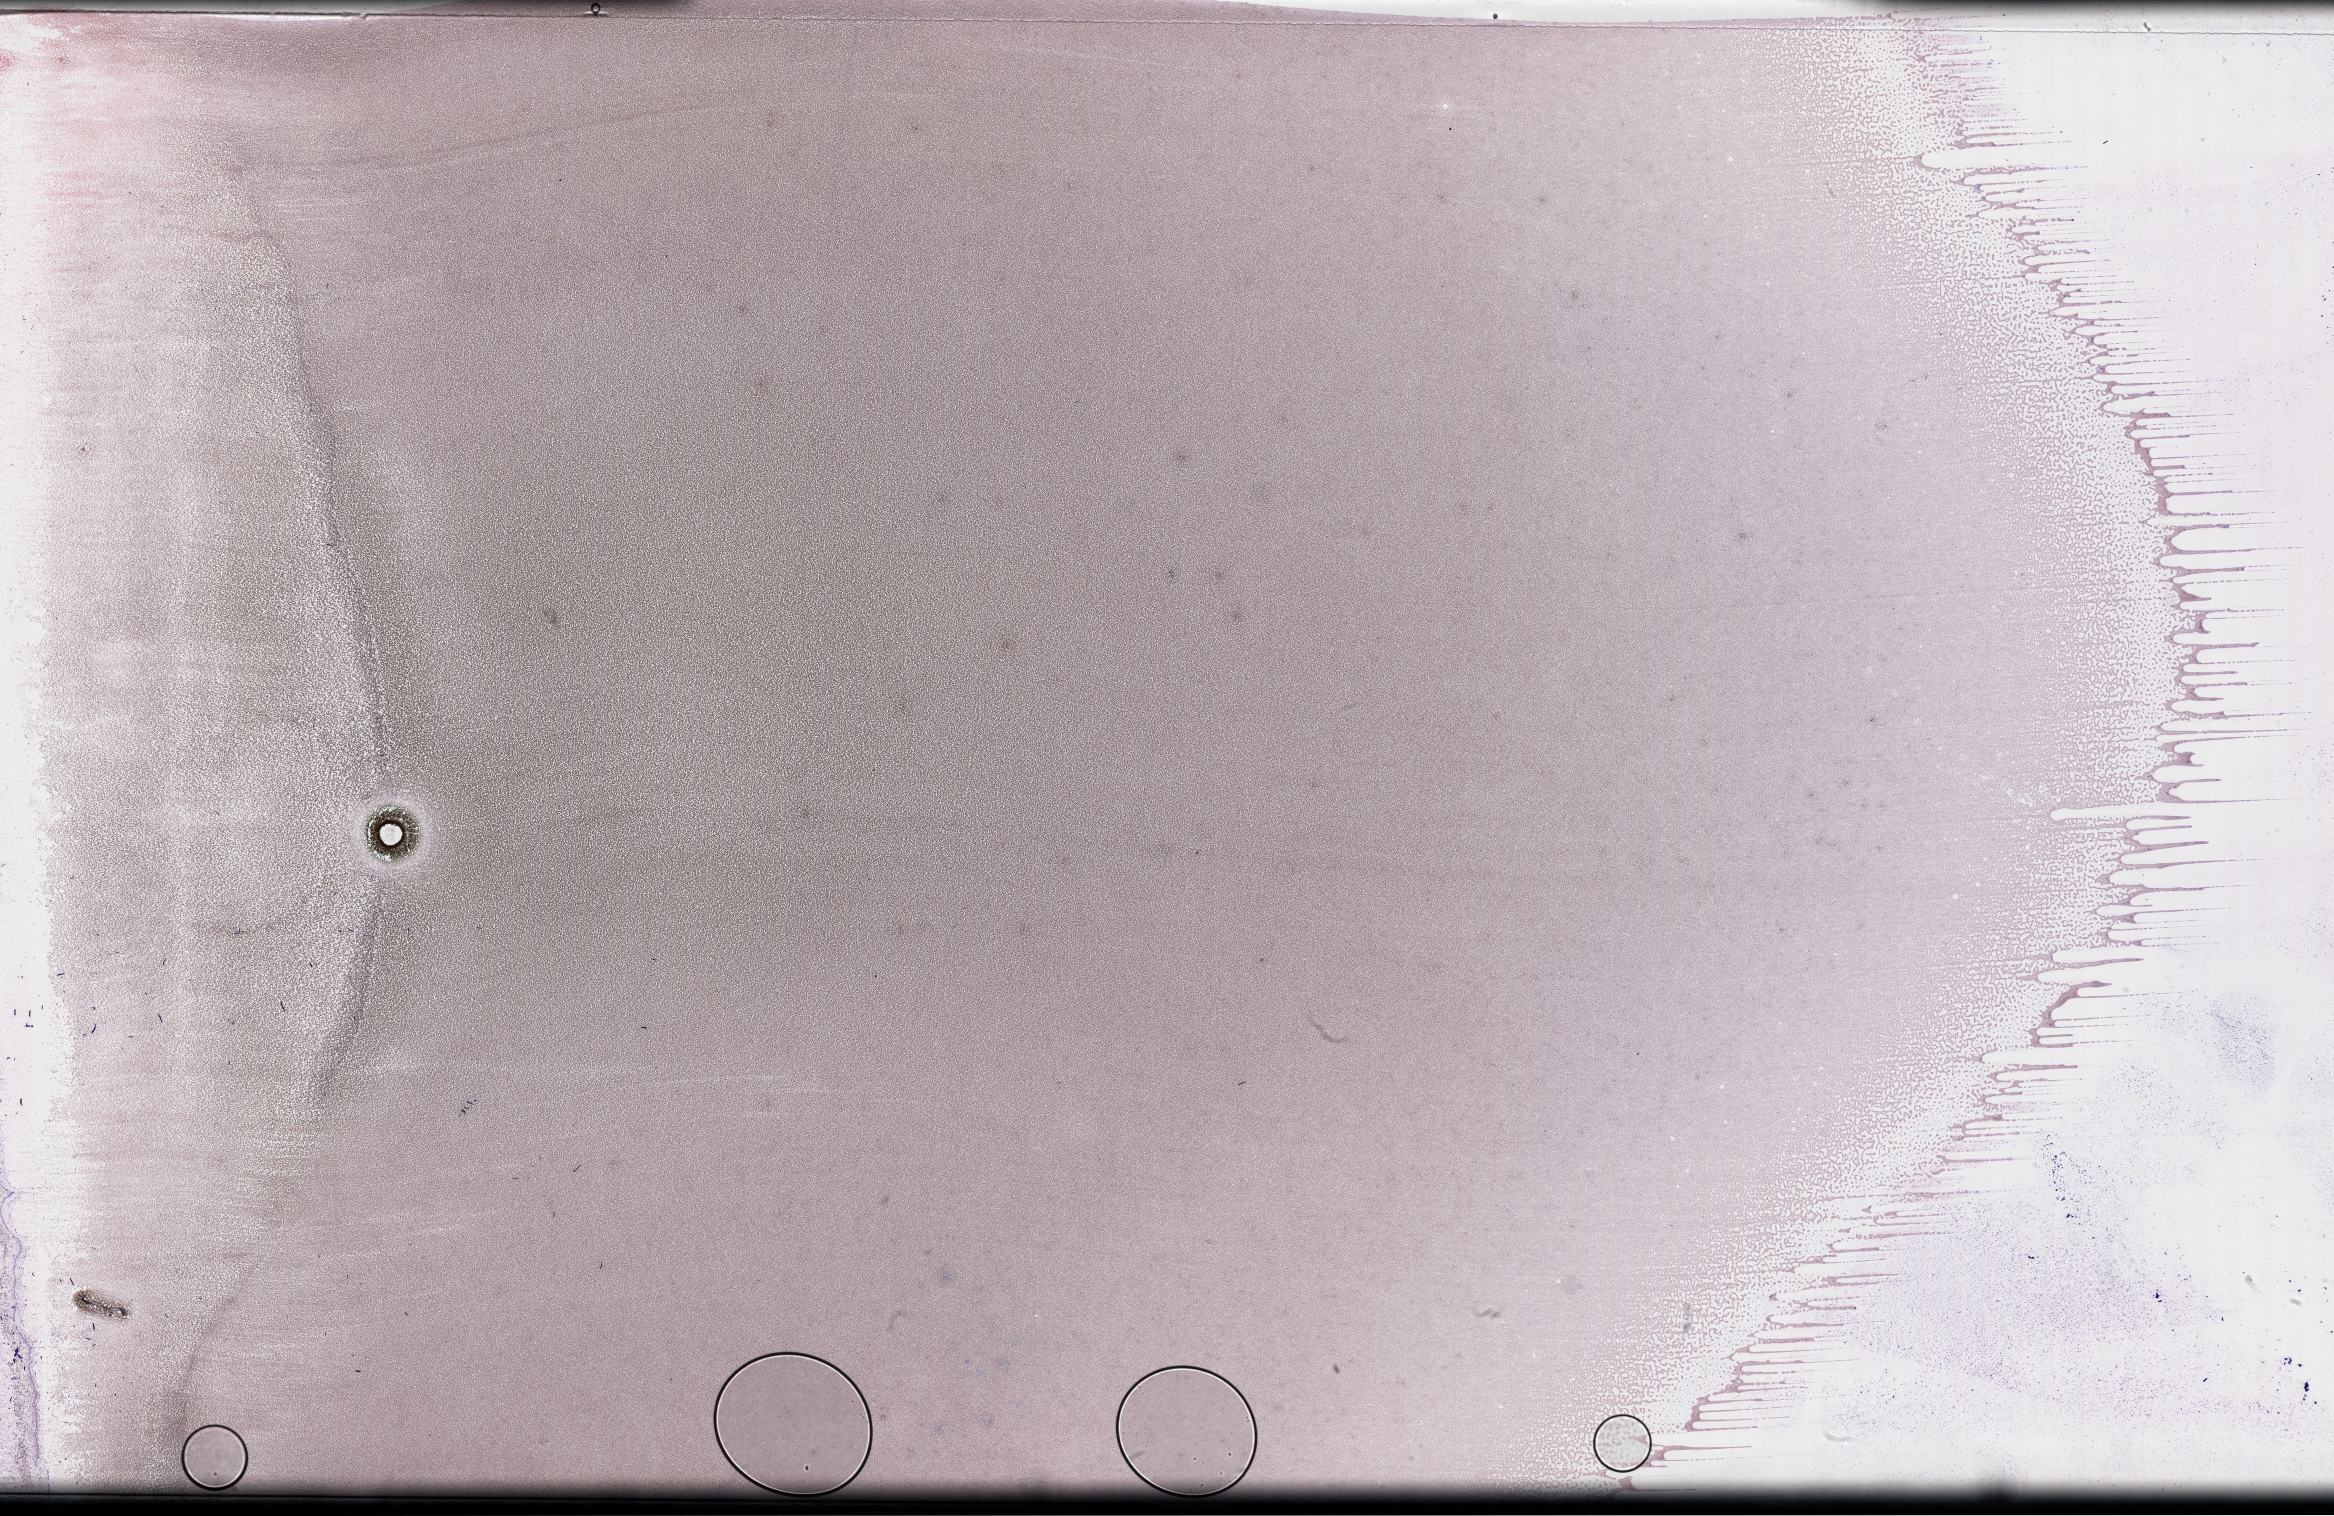
Whole-slide image of a whole blood smear, Wright–Giemsa stain, whole scanned area (about 37.7 x 24.5 mm) shown as a low-resolution overview; collected on treatment. Patient: male.
Patient diagnosis: Plasma Cell Myeloma.